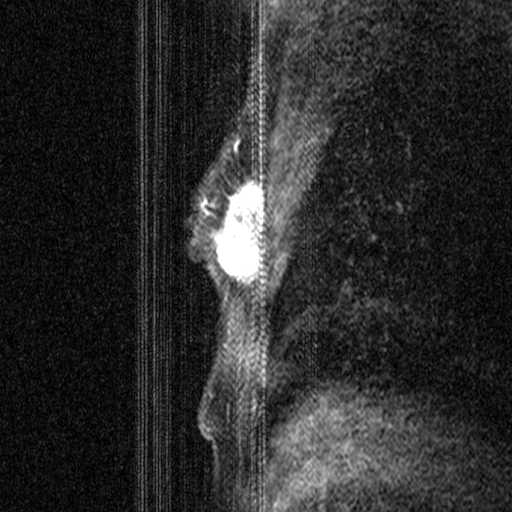
Breast MRI (dynamic contrast-enhanced), one sagittal slice. Dynamic contrast-enhanced study with each time point stored as its own series, time point 2 of 3 at this slice position (early post-contrast, ordered by acquisition time). 1.5 T. TE 4.5 ms, TR 11 ms. 3 mm slice thickness. 512 × 512 image matrix. Patient: female, 44 years. Case-level facts recorded for this patient, not image findings: setting: breast cancer imaged before/during neoadjuvant chemotherapy; receptor status: HR-positive, HER2-negative.
Annotated regions visible in this slice (semi-automatically segmented with operator editing):
- analysis volume of interest (the breast-tissue region the enhancement analysis was run in; not a lesion): bounding box [x1, y1, x2, y2] px = [206, 164, 265, 299]
- tumour enhancement mask (voxels above the 90 % enhancement threshold inside the analysis volume of interest): [206, 173, 264, 281]